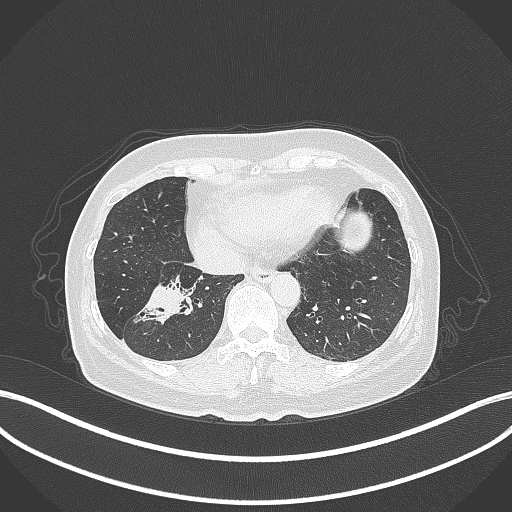
Chest CT, one axial slice; position 116 of 429 along the scan axis; 120 kVp; lung window (W 1500 / L -600 HU); 512 × 512 image matrix, field of view 400 × 400 mm. Female patient, age 67 years. Case-level facts recorded for this patient, not image findings: clinical TNM (as recorded): T1c N1 M0.
Structures marked on this image (rectangle marked by the reading radiologist):
- lung tumour (recorded histology: adenocarcinoma): bounding box <130,278,191,331> (left, top, right, bottom; pixels)